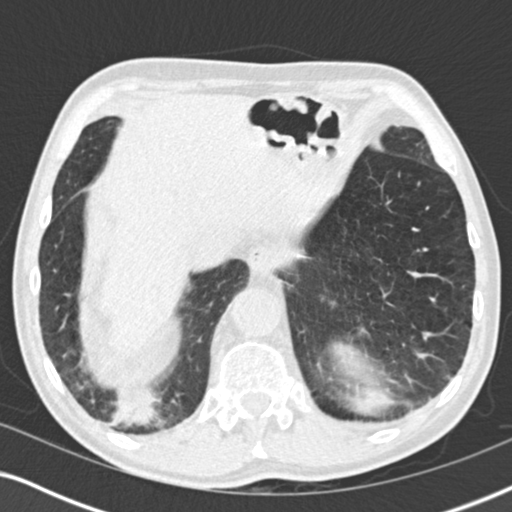
Low-dose screening chest CT, one axial slice; slice 50 of 196 in the series (ordered by position); 120 kVp; lung window (W 1500 / L -600 HU); 2 mm slice thickness; 512 × 512 image matrix, field of view 330 × 330 mm.
Structures marked on this image (expert manual segmentation):
- lesion 3 (tumor, lower lobe of right lung): box from (x=111, y=388) to (x=160, y=427) px